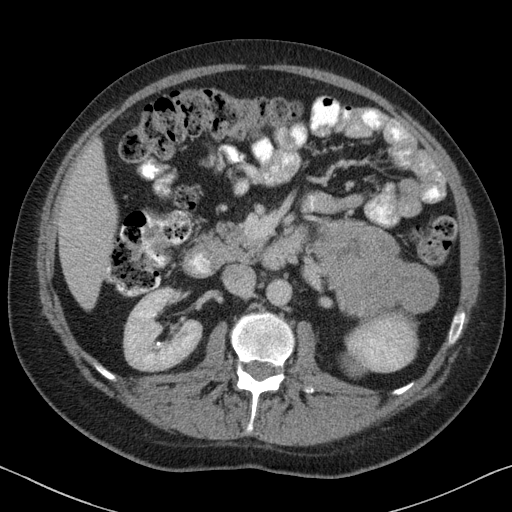
Contrast-enhanced abdominal CT, one axial slice; position 35 of 88 along the scan axis; reconstruction kernel B31f; intravenous contrast given; soft-tissue window (W 400 / L 40 HU); 3 mm slice thickness; 512 × 512 image matrix, field of view 366 × 366 mm. Patient: male, 51 years. Case-level facts recorded for this patient, not image findings: diagnosis: adrenocortical carcinoma; tumour side: left adrenal; tumour size at pathology: 16.5 cm; Ki-67 index: 30 %; stage (as recorded): 2.
Annotated regions visible in this slice (semi-automatically segmented with operator editing):
- mass: bounding box [x1, y1, x2, y2] px = [315, 222, 435, 373]